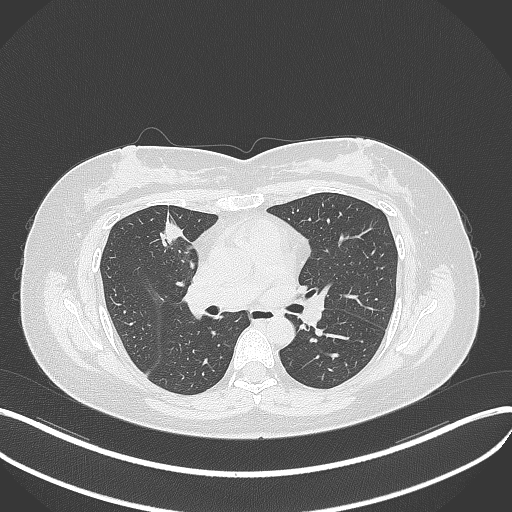
Chest CT, one axial slice. Position 177 of 273 along the scan axis. 120 kVp. Lung window (W 1500 / L -600 HU). 512 × 512 image matrix, field of view 400 × 400 mm. Patient: female, 42 years. Case-level facts recorded for this patient, not image findings: clinical TNM (as recorded): T1b N0 M0.
Structures marked on this image (rectangle marked by the reading radiologist):
- lung tumour (recorded histology: adenocarcinoma): bounding box (x1, y1, x2, y2) in pixels: (151, 213, 187, 250)